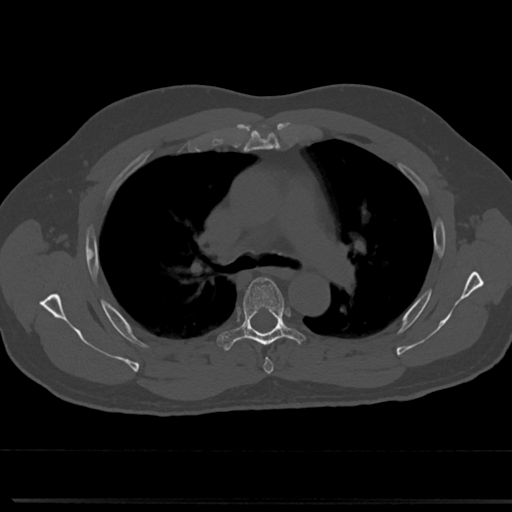
CT including the spine, one axial slice; position 506 of 817 along the scan axis; 120 kVp; bone window (W 1800 / L 400 HU); 0.5 mm slice thickness; 512 × 512 image matrix, field of view 355 × 355 mm. Patient: male, 61 years. From the clinical record (not read from this slice): primary cancer: prostate.
Annotated regions visible in this slice (semi-automatically segmented with operator editing):
- T4 vertebra: box from (x=262, y=345) to (x=273, y=374) px
- T5 vertebra: (x=218, y=276)–(x=310, y=352)